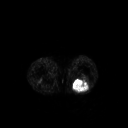
FDG PET of an extremity soft-tissue mass (from a PET/CT study), one axial slice. Position 190 of 267 along the scan axis. 128 × 128 image matrix, field of view 500 × 500 mm. Patient: male, 54 years. From the clinical record (not read from this slice): histological type: synovial sarcoma; site of the primary tumour: left poplietal fossa.
Outlined on this slice (expert contour drawn on MRI and transferred to this co-registered scan by the dataset authors):
- gross tumour volume (mass): box from (x=71, y=78) to (x=90, y=93) px